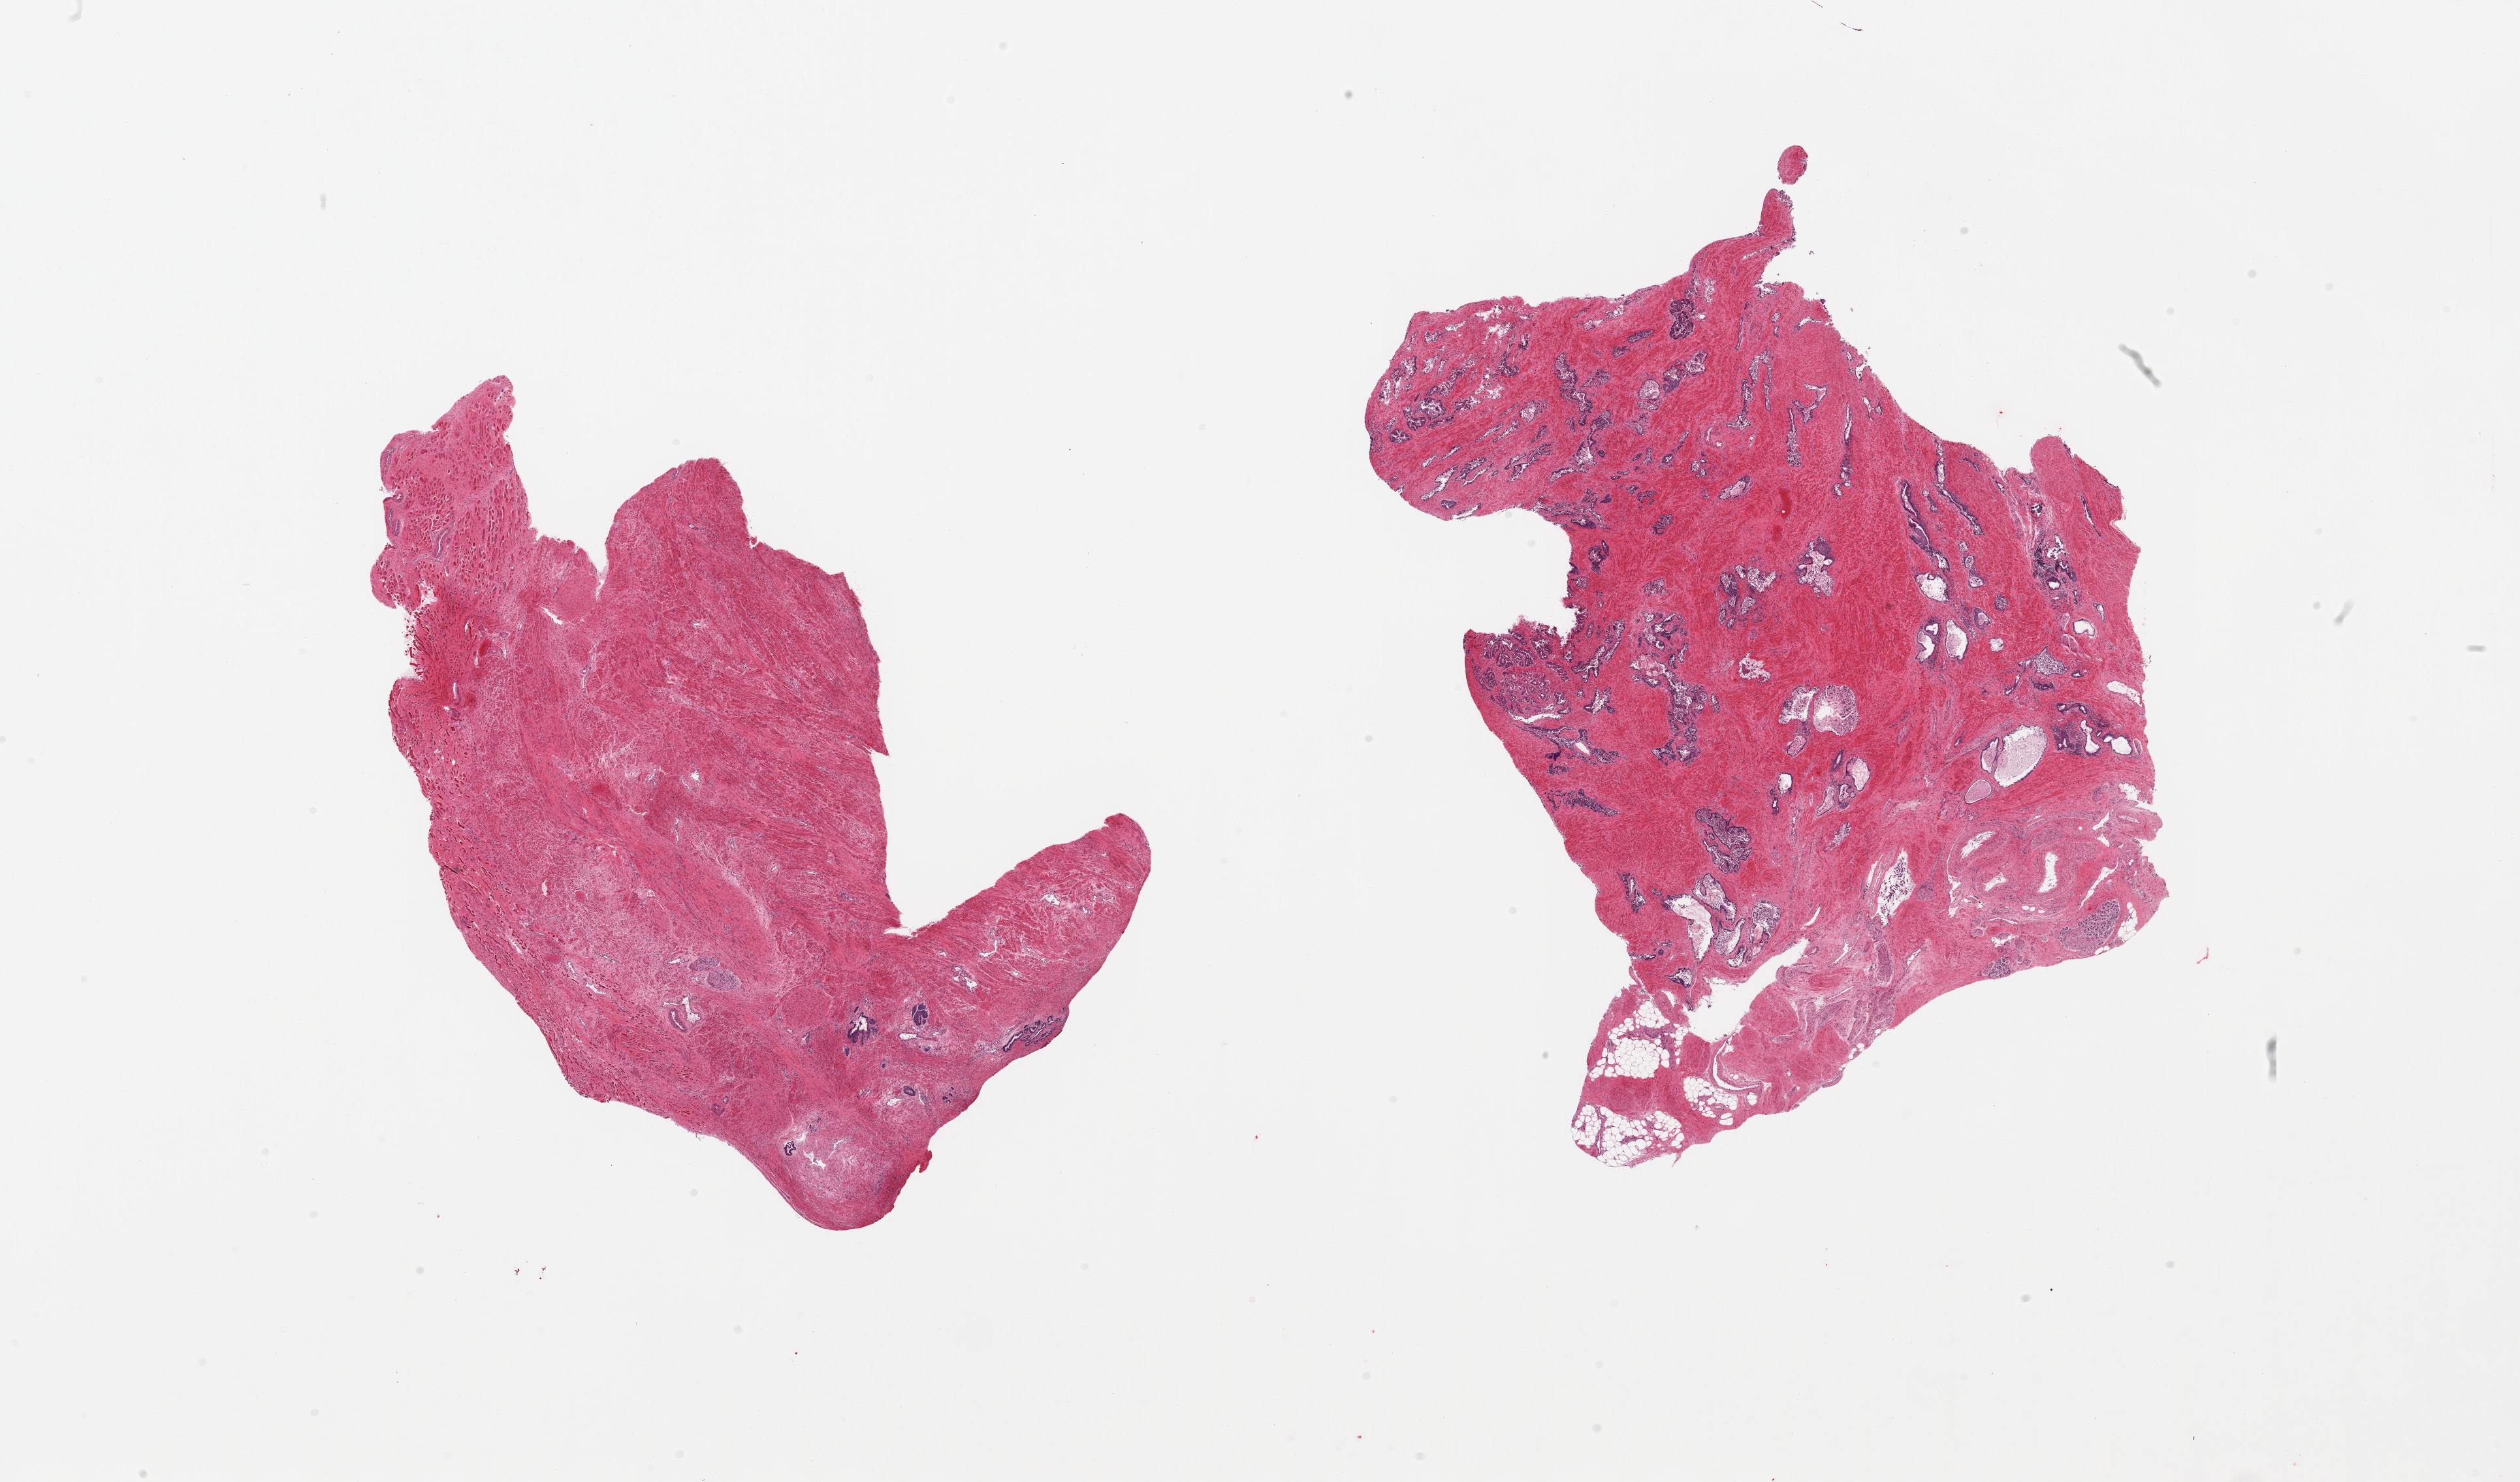
H&E whole-slide image, shown as a low-resolution overview of the whole scanned area (about 30.5 x 18.0 mm, from a 20x scan). PAXgene-fixed paraffin-embedded (PFPE) section. Section of prostate (target tissue). Tissue donor sample. Male donor.
Pathologist's review note for this sample: 2 pieces glandular mucosa moderately autolyzed; One aliquot largely stroma, rare glands.